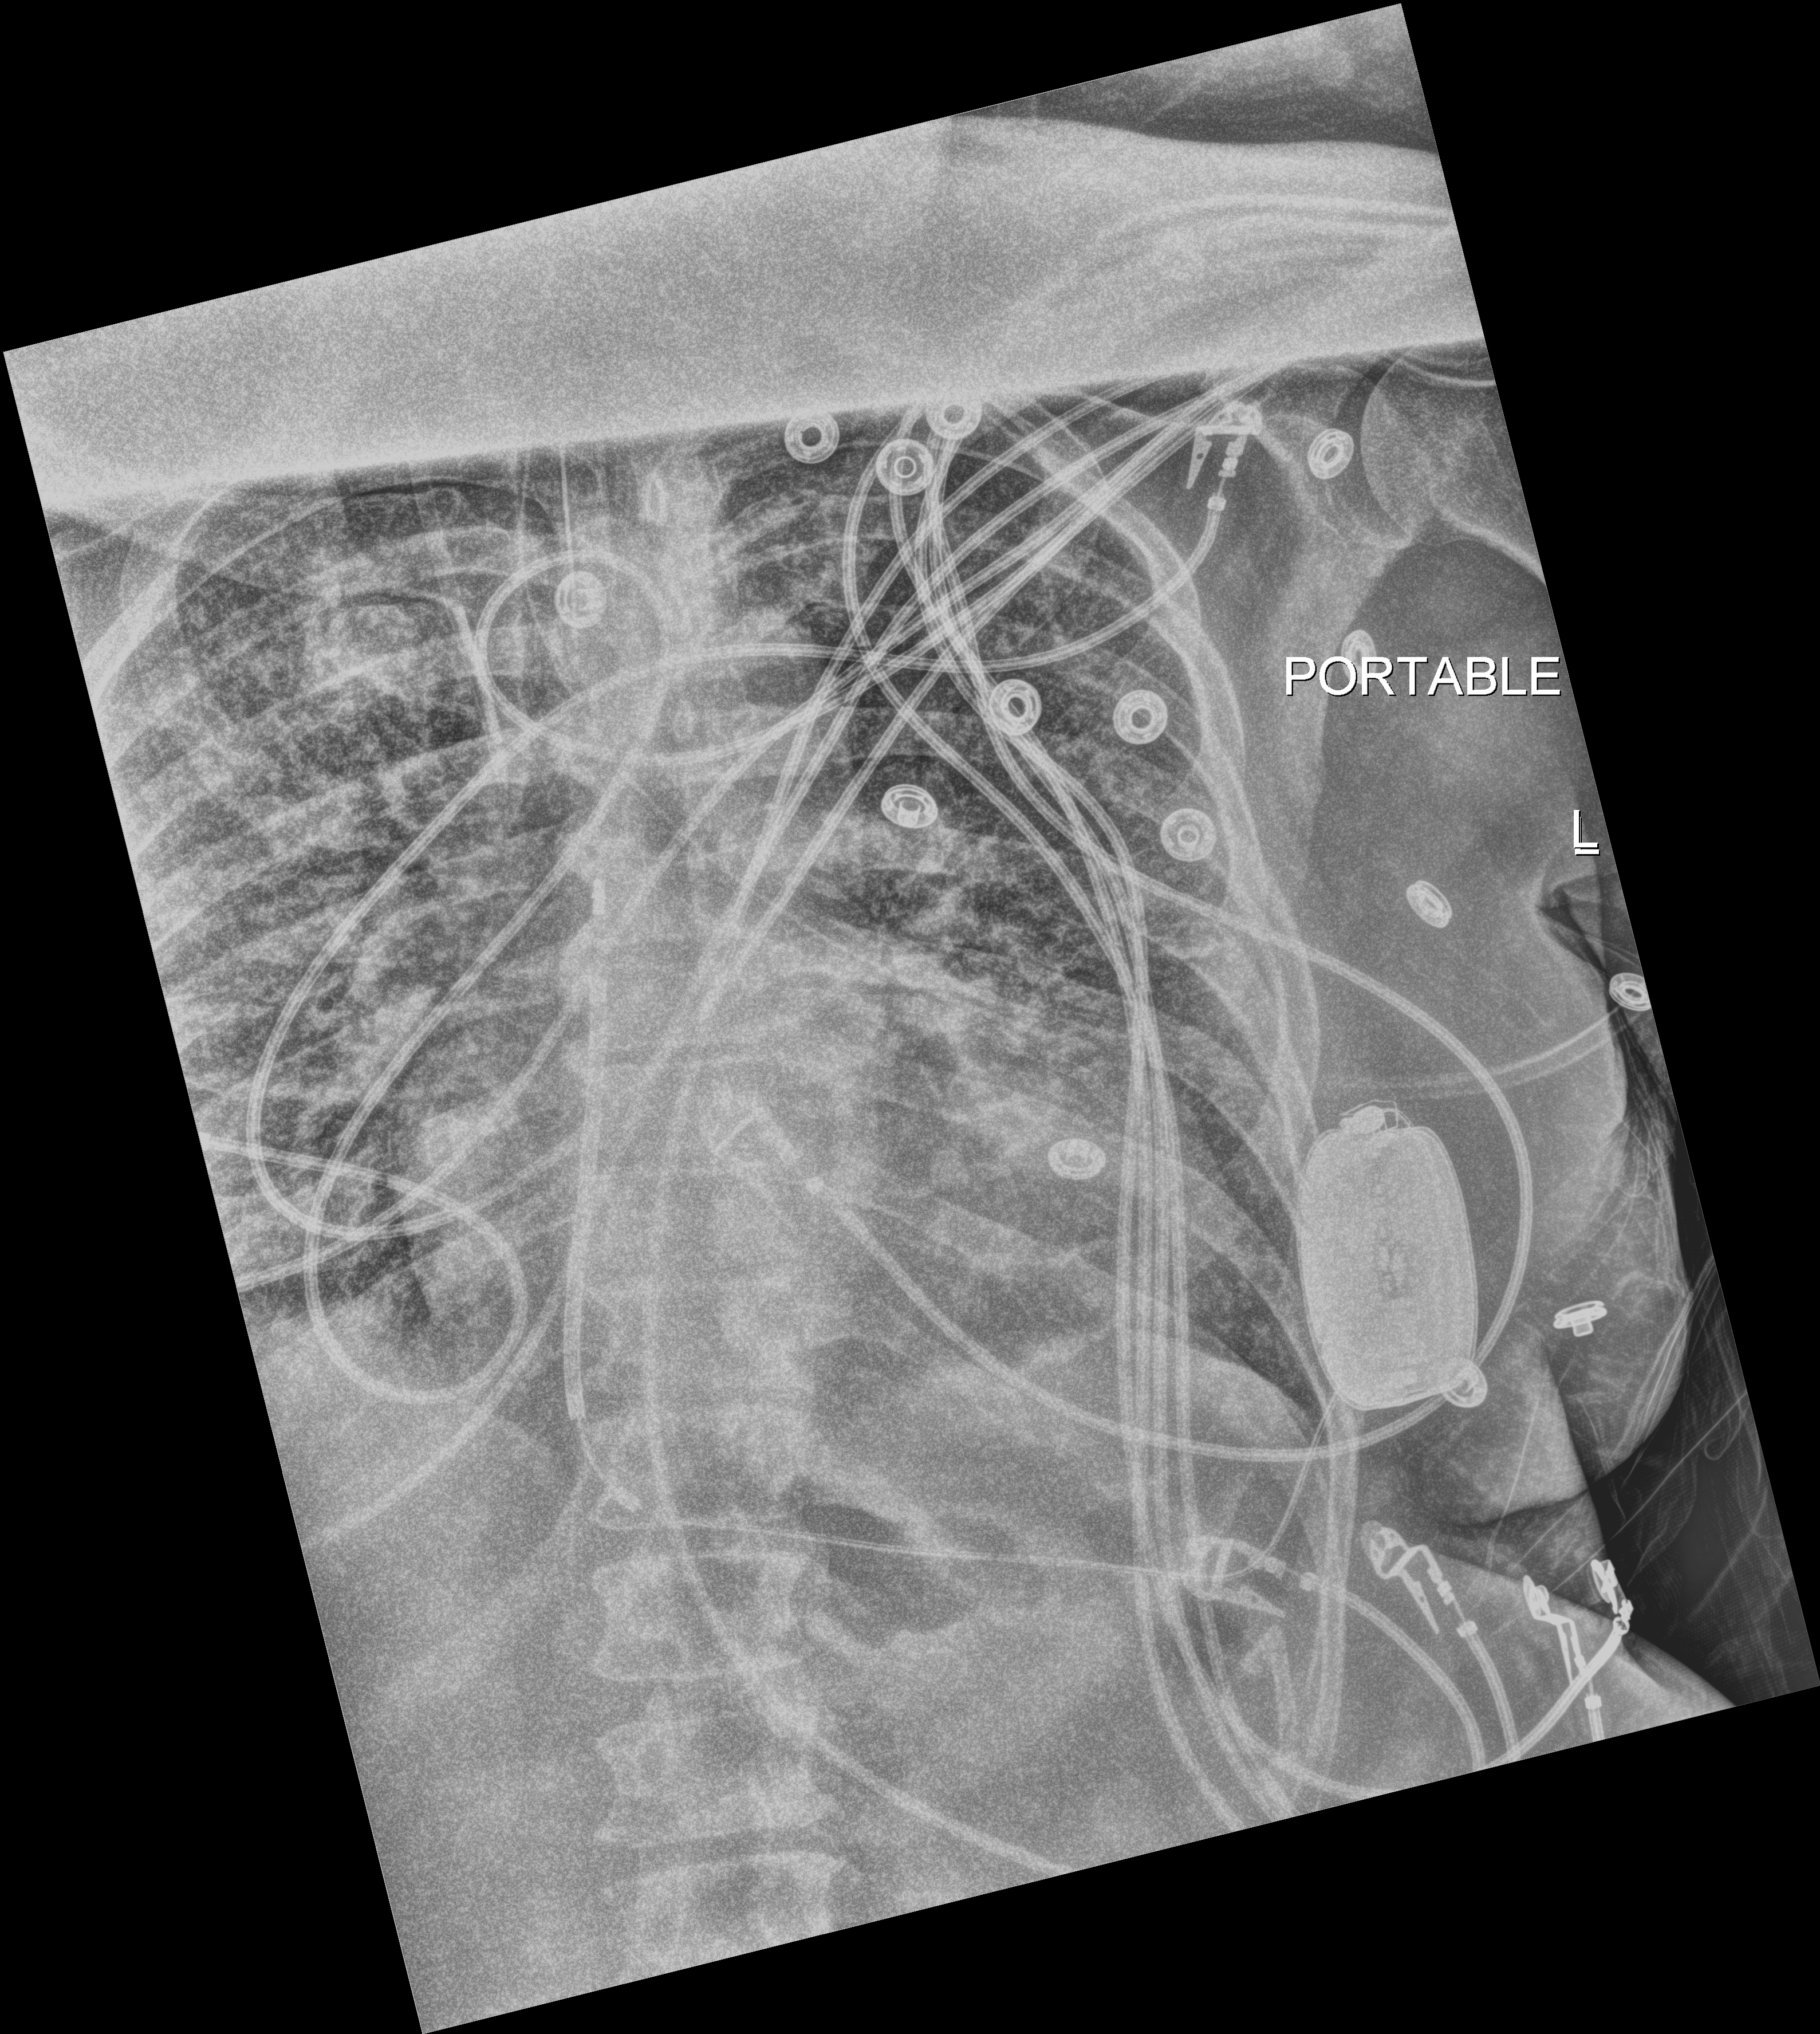
Portable chest radiograph; anteroposterior (AP) projection. Patient hospitalised with COVID-19; male, aged 60–74 years.
From the hospital-stay record, not from the radiograph (when in the stay this image was taken is not recorded): mechanically ventilated during this hospital stay: yes; chronic kidney disease (admission record): no.